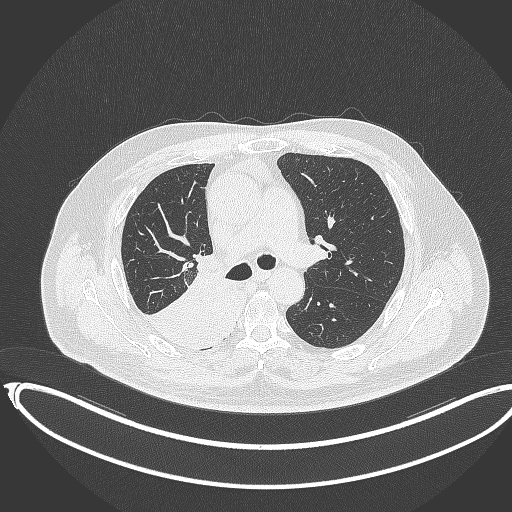
Chest CT, one axial slice. Position 228 of 403 along the scan axis. 120 kVp. Lung window (W 1500 / L -600 HU). 1 mm slice thickness. 512 × 512 image matrix. Patient: male, 68 years. Case-level facts recorded for this patient, not image findings: clinical TNM (as recorded): T2a N0 M0.
Structures marked on this image (rectangle marked by the reading radiologist):
- lung tumour (recorded histology: adenocarcinoma): box from (x=138, y=254) to (x=228, y=342) px